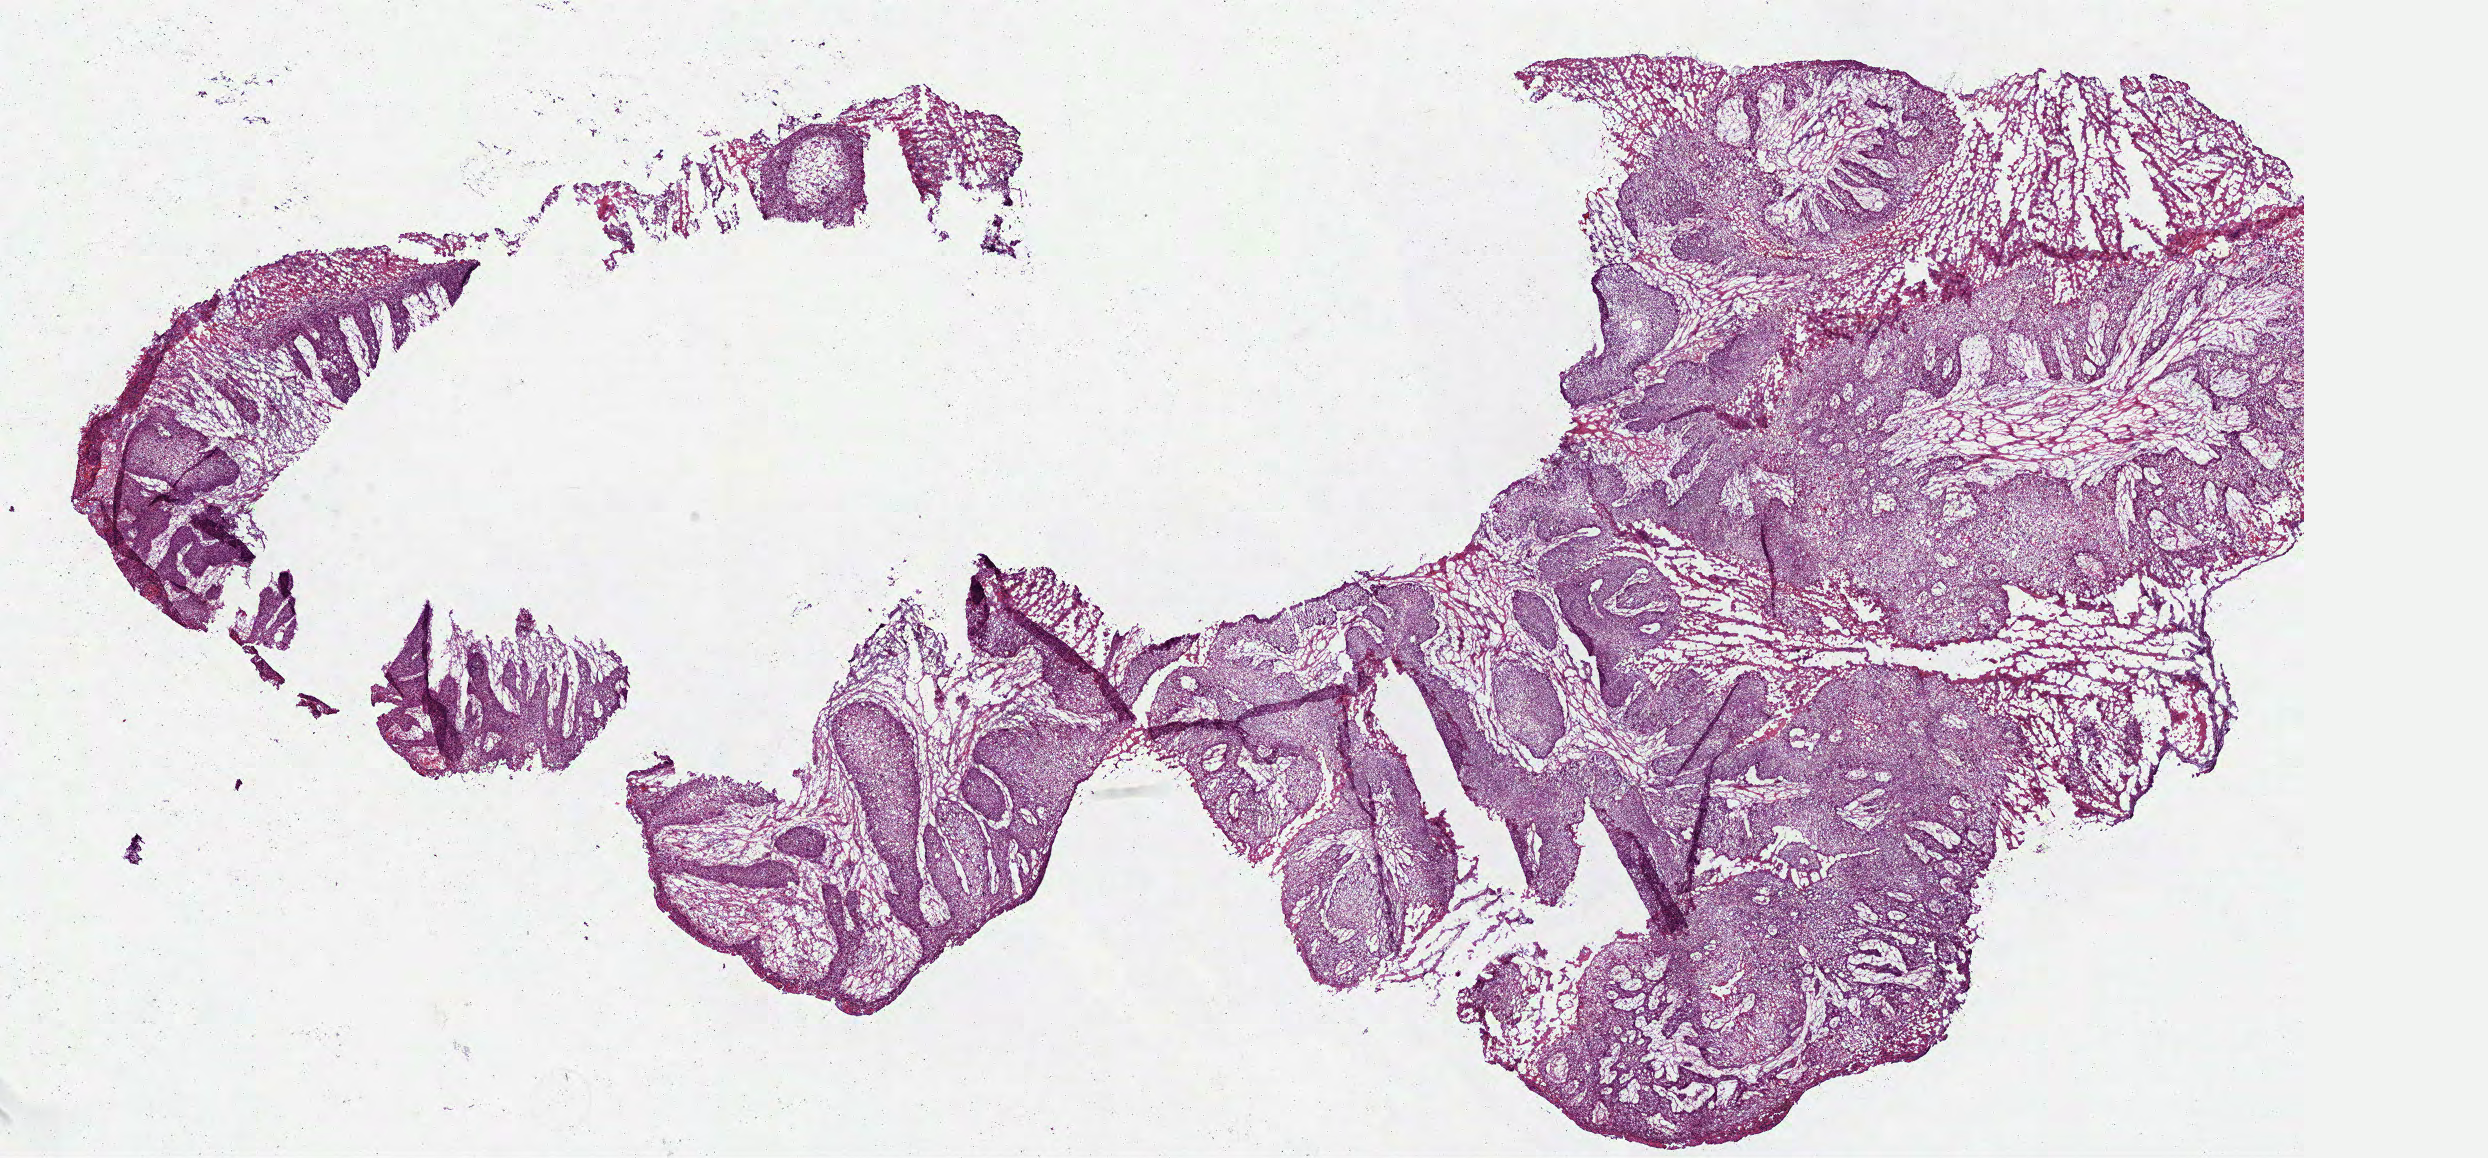
Digitized Hematoxylin and eosin (H&E) stained tissue section (whole slide) — whole scanned area (about 20.1 x 9.3 mm, from a 40x scan) shown as a low-resolution overview, frozen section, sample: primary tumour, lung. Male, age 66 years at initial diagnosis. Composition of this section per pathologist review: tumour cells 70%, tumour nuclei 70%, normal cells 0%, stromal cells 20%, necrosis 10%. Inflammatory infiltration, as recorded: lymphocyte infiltration 10%, neutrophil infiltration 5%.
- AJCC pathologic stage: IA
- diagnosis: Papillary squamous cell carcinoma (lower lobe, lung)